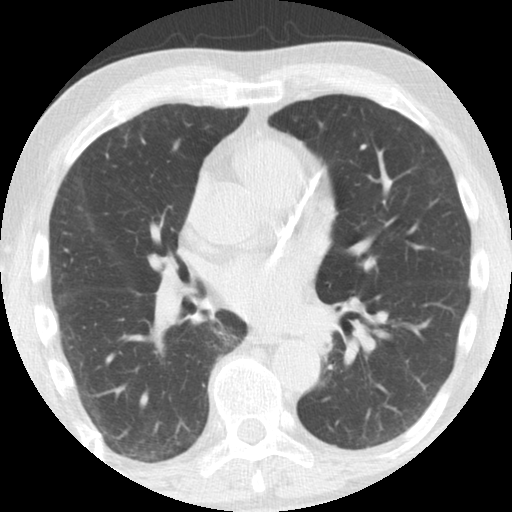
Chest CT (low-dose screening protocol), one axial image, third annual screen, lung window (W 1500 / L -600 HU), 2.5 mm slice thickness, 512 × 512 image matrix, field of view 308 × 308 mm. Male, age 61 years at enrolment. Former smoker at enrolment.
Lesion marked by an expert reader, box from (x=296, y=317) to (x=344, y=363) px. Screening reader's record for this exam: no non-calcified nodule ≥4 mm recorded. Official screen result: negative screen, minor abnormalities not suspicious for lung cancer. Participant outcome: lung cancer diagnosed 363 days after this screen — squamous cell carcinoma, NOS, left upper lobe, left lower lobe, well differentiated (G1), stage IIB (AJCC 6th edition), 100 mm at pathology.